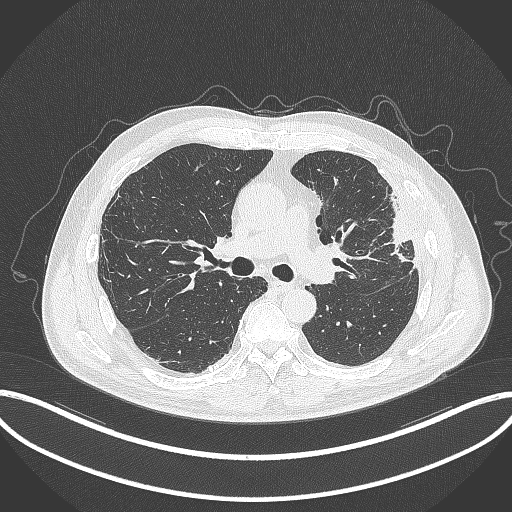
Chest CT, one axial slice; position 206 of 382 along the scan axis; reconstruction kernel B70f; lung window (W 1500 / L -600 HU); 1 mm slice thickness; 512 × 512 image matrix, field of view 415 × 415 mm. Male patient, age 64 years. Case-level facts recorded for this patient, not image findings: clinical TNM (as recorded): T4 N1 M0; histopathological grade: G3.
Structures marked on this image (rectangle marked by the reading radiologist):
- lung tumour (recorded histology: adenocarcinoma): box from (x=375, y=190) to (x=417, y=268) px